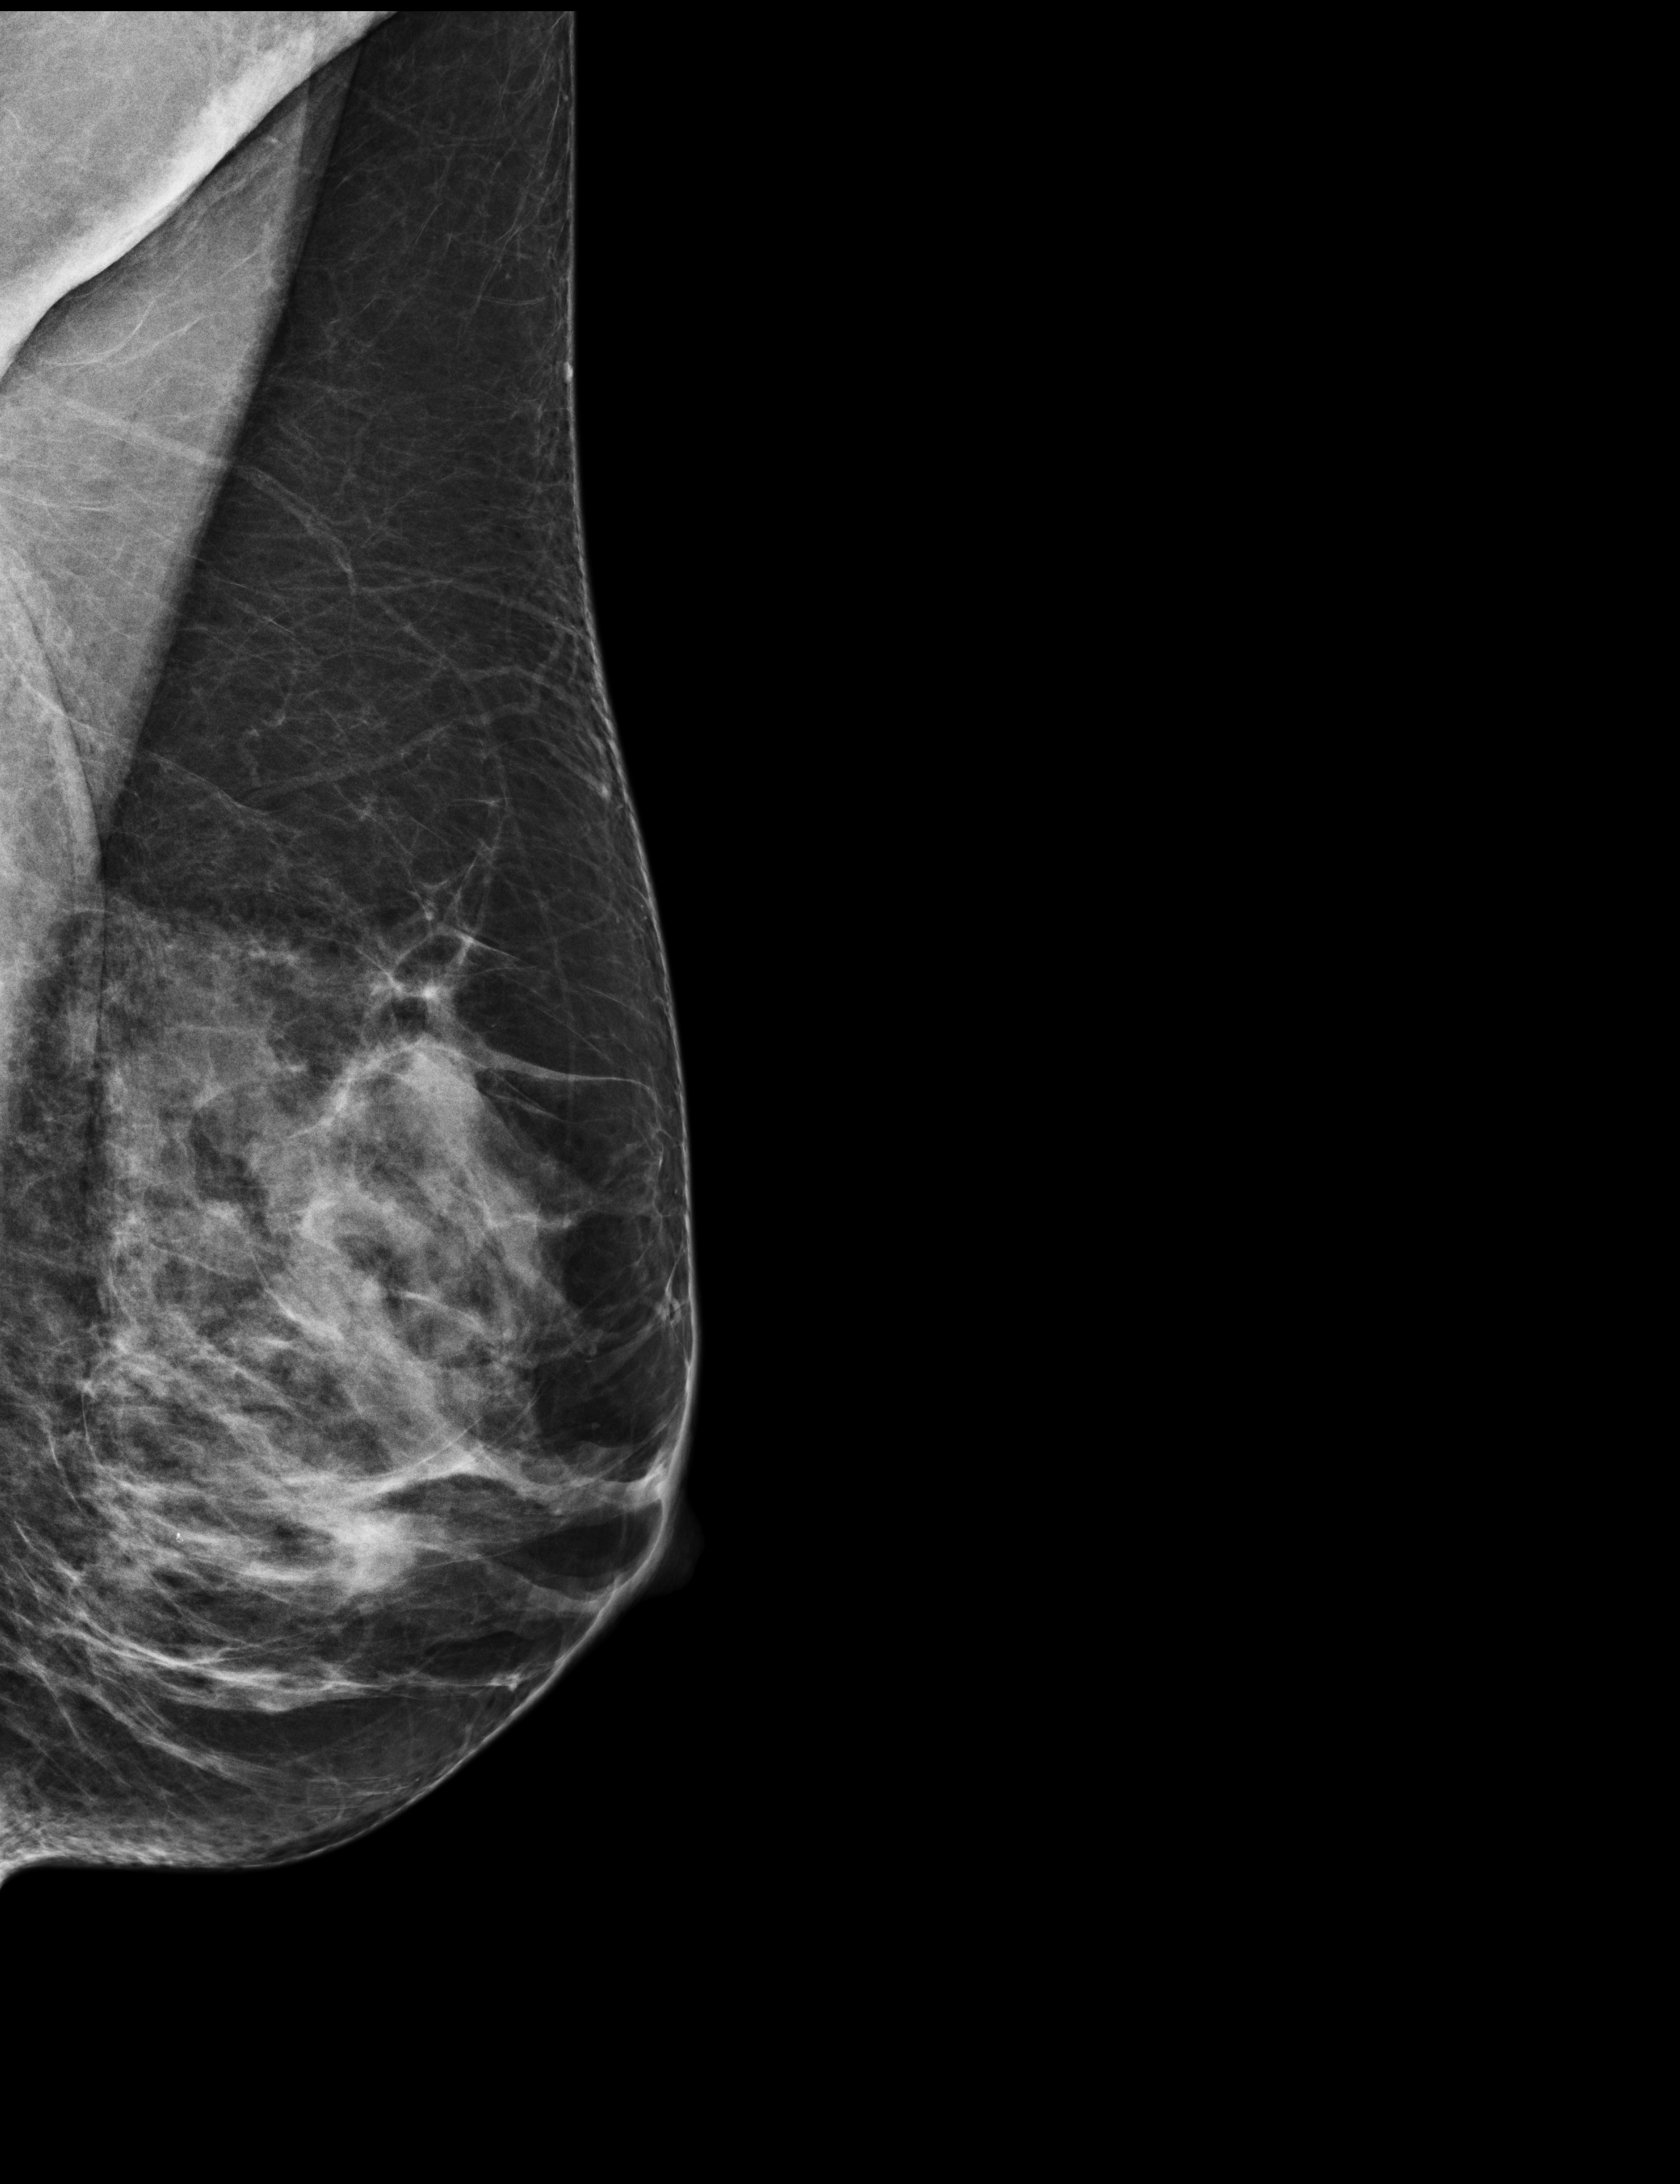
Full-field digital mammogram (FFDM); left breast; medio-lateral oblique projection; screening examination; system: Selenia Dimensions. Patient aged 59 years (female).
BI-RADS breast density category at the screening exam (both breasts, scale 1–4): 3. Final BI-RADS assessment for this screening round (tomosynthesis exam, both breasts): category 2. Recall: no recall after this screen.